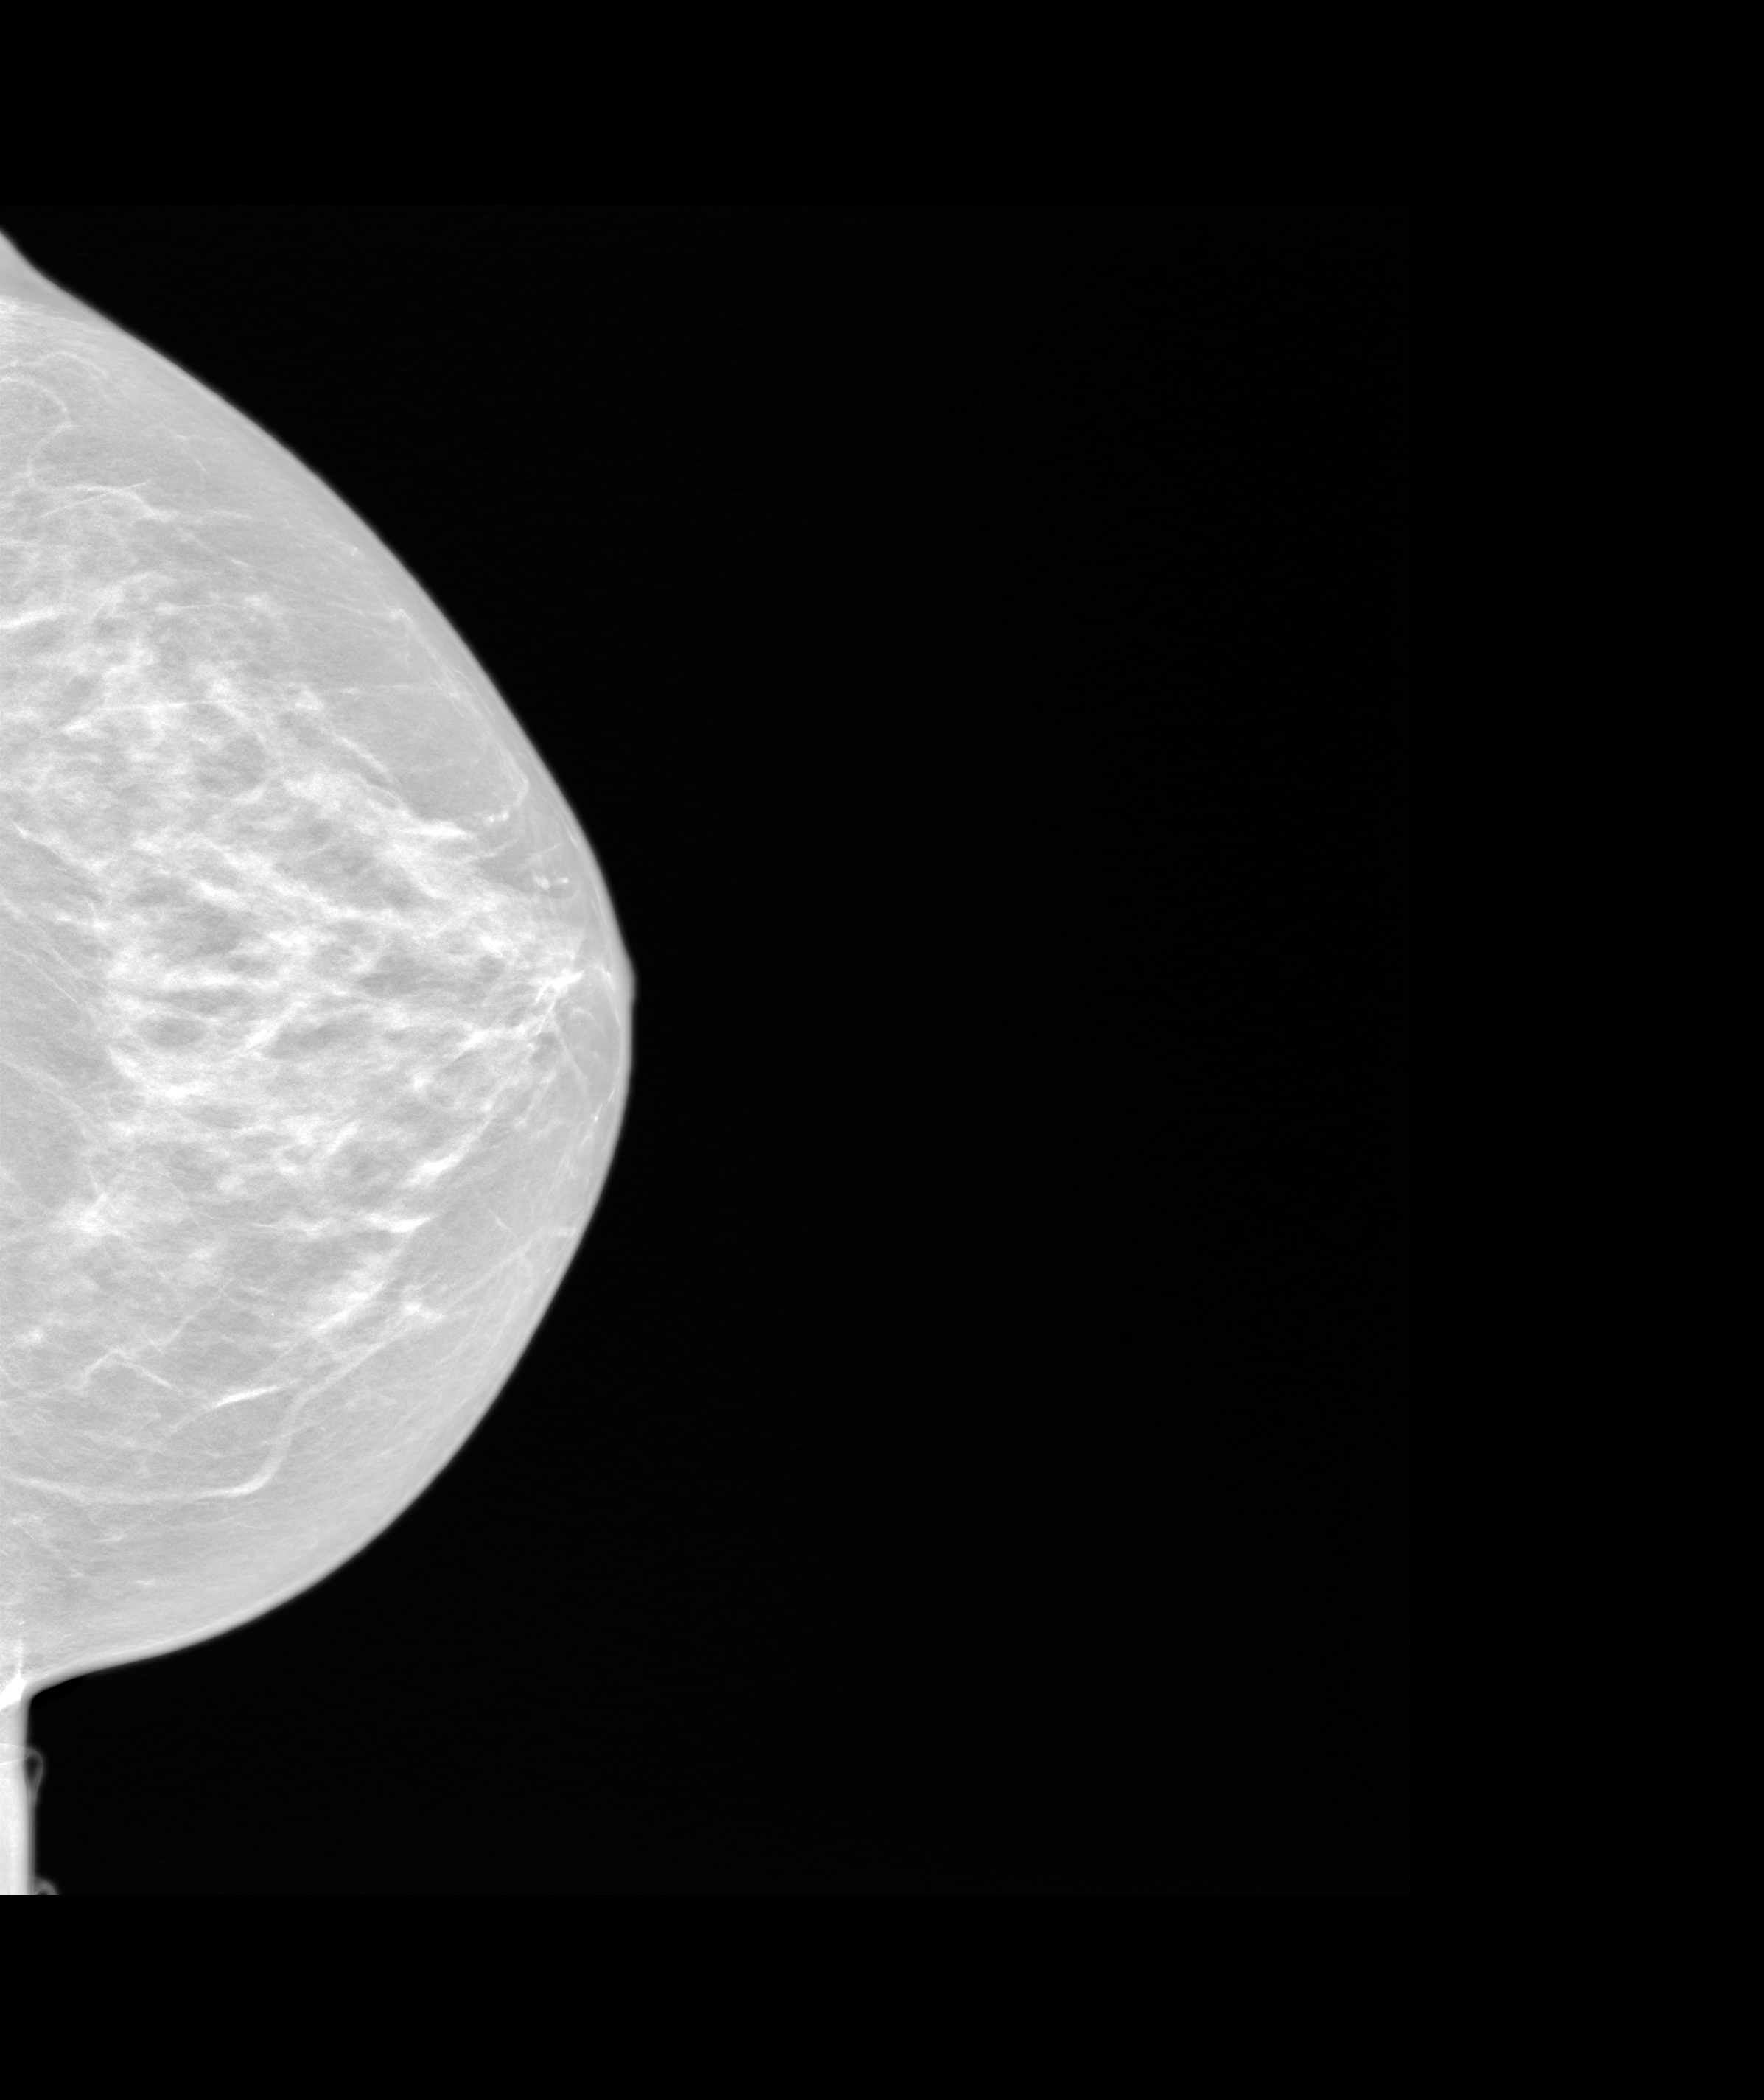
Annual screening mammography examination. Patient aged 59 years (female).
Image type: synthesized 2-D view from tomosynthesis. Breast: left. Projection: cranio-caudal projection.